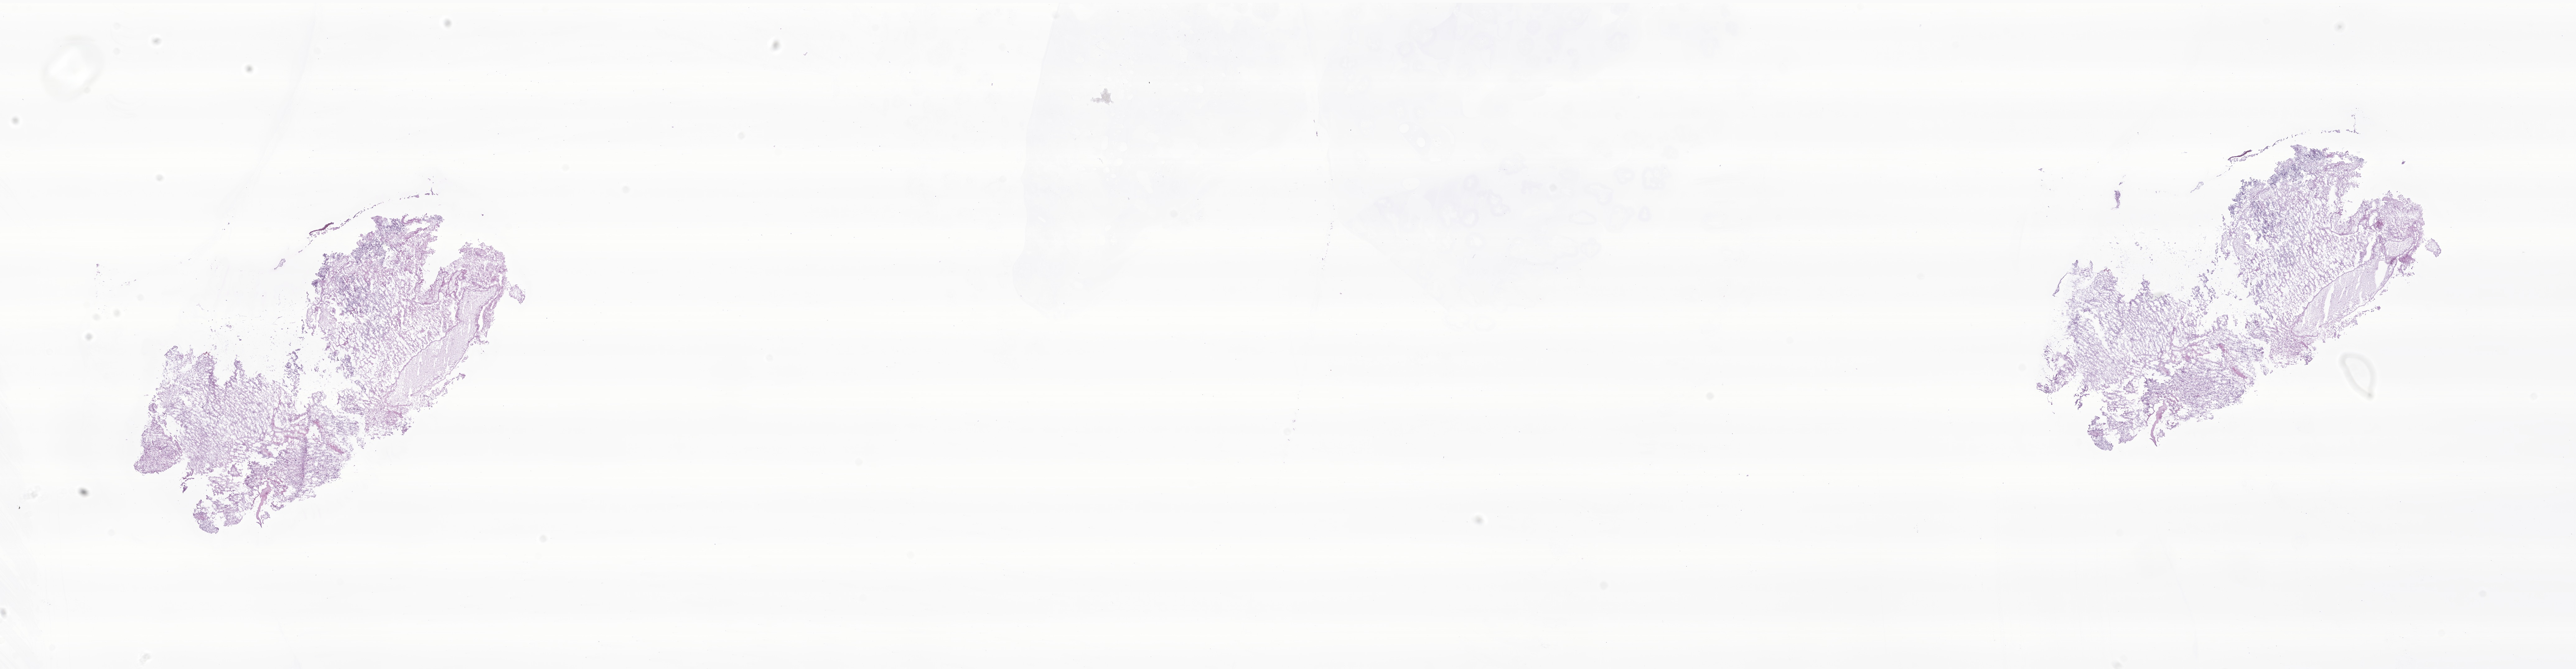
Digitized hematoxylin and eosin (H&E)-stained section of tumor tissue from the brain — whole scanned area (about 34.9 x 9.1 mm) shown as a low-resolution overview. Patient: male, age 142 months (11 years 10 months).
* specimen: frozen section (OCT-embedded)